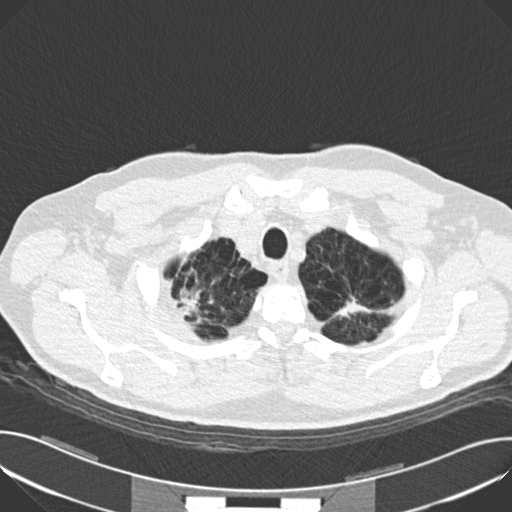
Low-dose screening chest CT, one axial slice. Slice 144 of 159 in the series (ordered by position). Reconstruction kernel B30f. 120 kVp. Lung window (W 1500 / L -600 HU). 2 mm slice thickness. 512 × 512 image matrix.
Annotated regions visible in this slice (expert manual segmentation):
- lesion 1 (tumor, upper lobe of right lung): box from (x=177, y=288) to (x=200, y=314) px